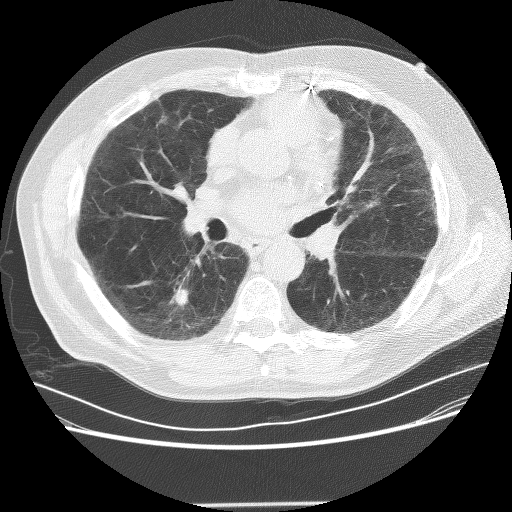
Axial slice from a low-dose chest CT screening exam; first (baseline) screen; lung window (W 1500 / L -600 HU); 2.5 mm slice thickness; lung (sharp) reconstruction kernel (BONE); slice 126 of 281 in the series; 512 × 512 image matrix, field of view 370 × 370 mm. Male participant, aged 72 years at enrolment. Former smoker at enrolment.
Lesion marked by an expert reader, bounding box [x1, y1, x2, y2] px = [148, 273, 202, 322]. The screening reader recorded 2 non-calcified nodules or masses ≥4 mm on this exam; which of them this box marks is not recorded. Official screen result: positive, change unspecified: nodule(s) >= 4 mm or enlarging nodule(s), mass(es), or other non-specific abnormalities suspicious for lung cancer. Later outcome: lung cancer diagnosed 436 days after this screen (after the second annual screen) — squamous cell carcinoma, NOS, right lower lobe, poorly differentiated (G3), stage IB (AJCC 6th edition), 42 mm at pathology.